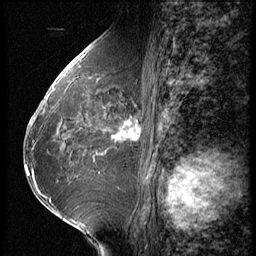
Breast MRI (dynamic contrast-enhanced), one sagittal slice. Position 29 of 62 along the scan axis. 3 images stored at this slice position (order not interpretable as contrast timing). 1.5 T. TE 4.2 ms, TR 9 ms. 2.5 mm slice thickness. 256 × 256 image matrix, field of view 180 × 180 mm. Patient: female, 65 years. Case-level facts recorded for this patient, not image findings: setting: breast cancer imaged before/during neoadjuvant chemotherapy; receptor status: HR-positive, HER2-negative.
Structures marked on this image (semi-automatically segmented with operator editing):
- analysis volume of interest (the breast-tissue region the enhancement analysis was run in; not a lesion): bounding box (x1, y1, x2, y2) in pixels: (104, 104, 154, 161)
- tumour enhancement mask (voxels above the 140 % enhancement threshold inside the analysis volume of interest): (115, 116, 133, 139)